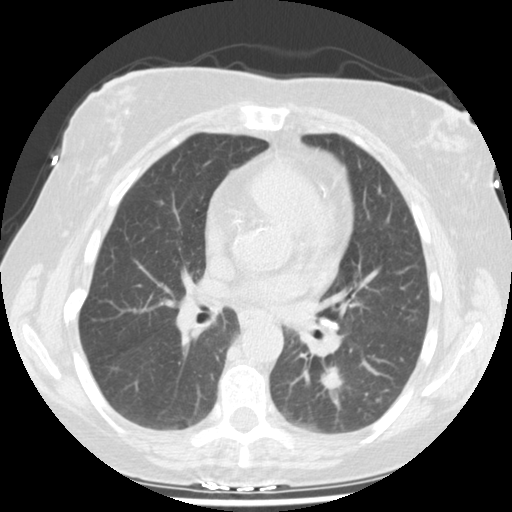
Chest CT (low-dose screening protocol), one axial image, second annual screen, lung window (W 1500 / L -600 HU), 2.5 mm slice thickness, standard (soft-tissue) reconstruction kernel (STANDARD), 120 kVp, slice 68 of 159 in the series. Female, age 61 years at enrolment. Current smoker at enrolment.
Expert reader's lesion annotation, bounding box [x1, y1, x2, y2] px = [312, 353, 361, 406]. The screening reader recorded 2 non-calcified nodules or masses ≥4 mm on this exam (left lower lobe, right upper lobe); which of them this box marks is not recorded. Official screen result: positive, change unspecified: nodule(s) >= 4 mm or enlarging nodule(s), mass(es), or other non-specific abnormalities suspicious for lung cancer. Participant outcome: lung cancer diagnosed 69 days after this screen — squamous cell carcinoma, NOS, left lower lobe, moderately differentiated (G2), stage IA (AJCC 6th edition), 12 mm at pathology.